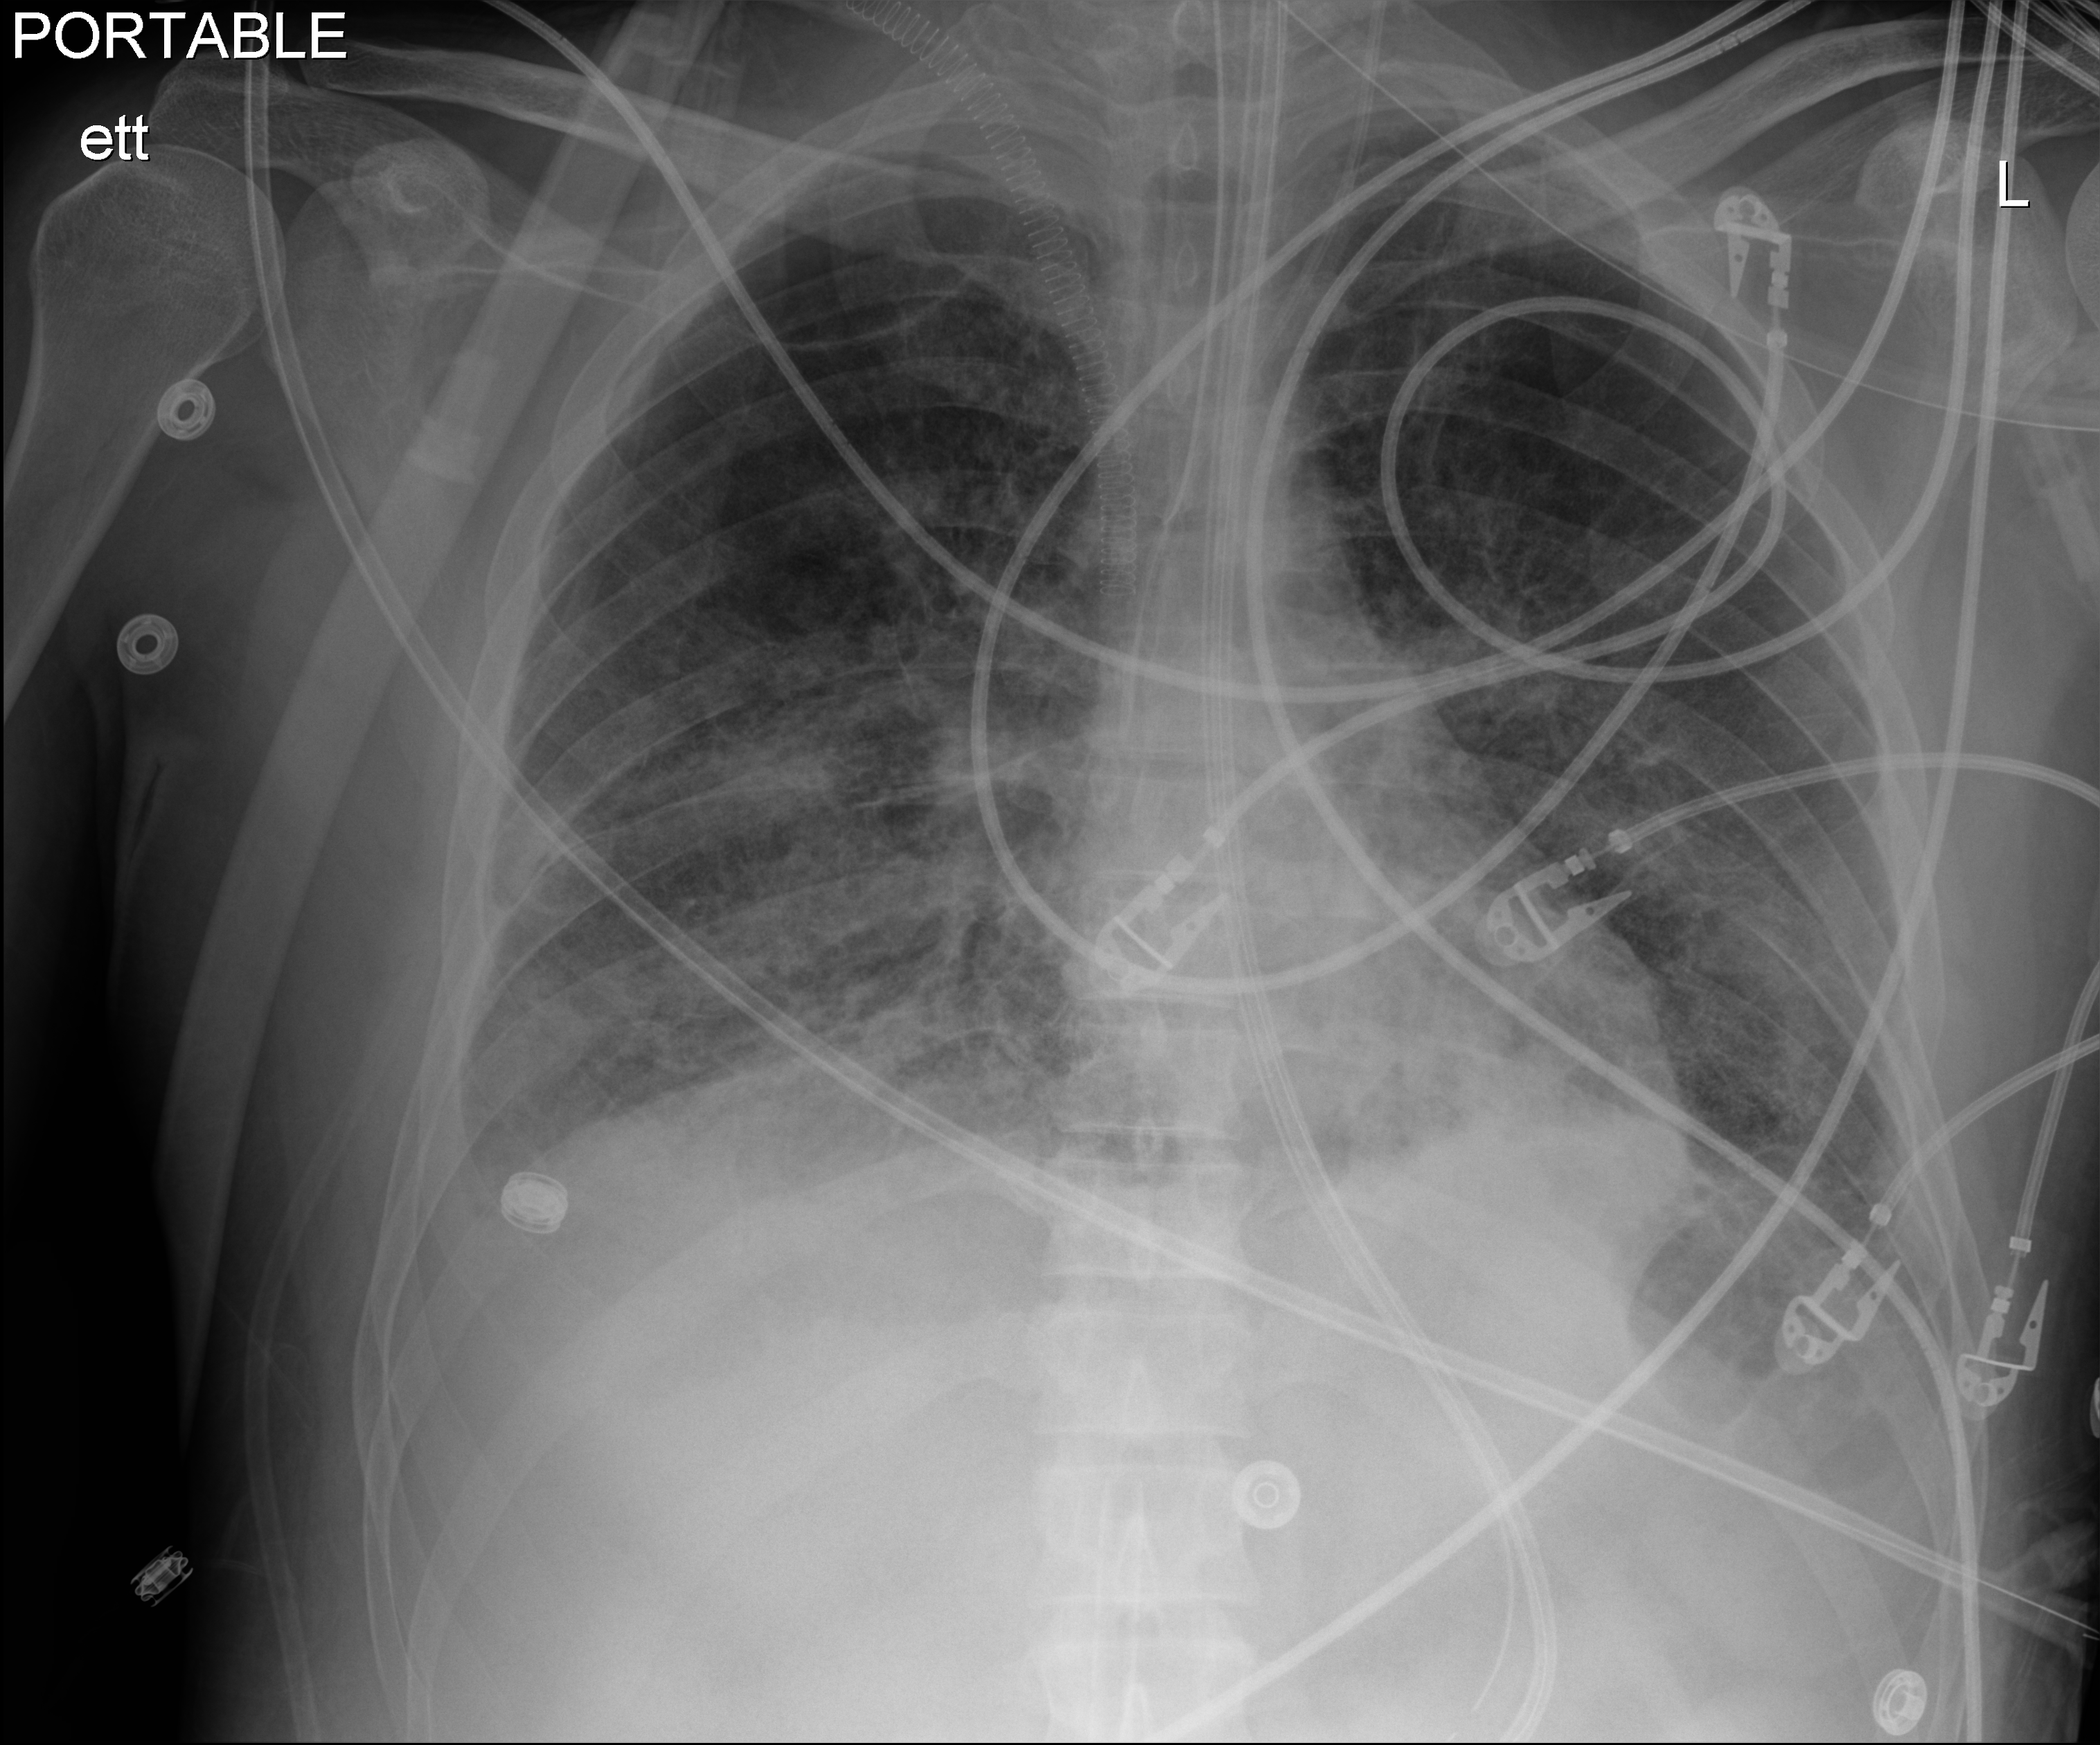
Bedside chest radiograph (digital radiography); anteroposterior (AP) projection. Adult patient hospitalised with COVID-19, age 18–59 years.
Admission-level facts for this patient (not findings on this image; timing relative to this image not recorded):
- length of hospital stay: 60 days